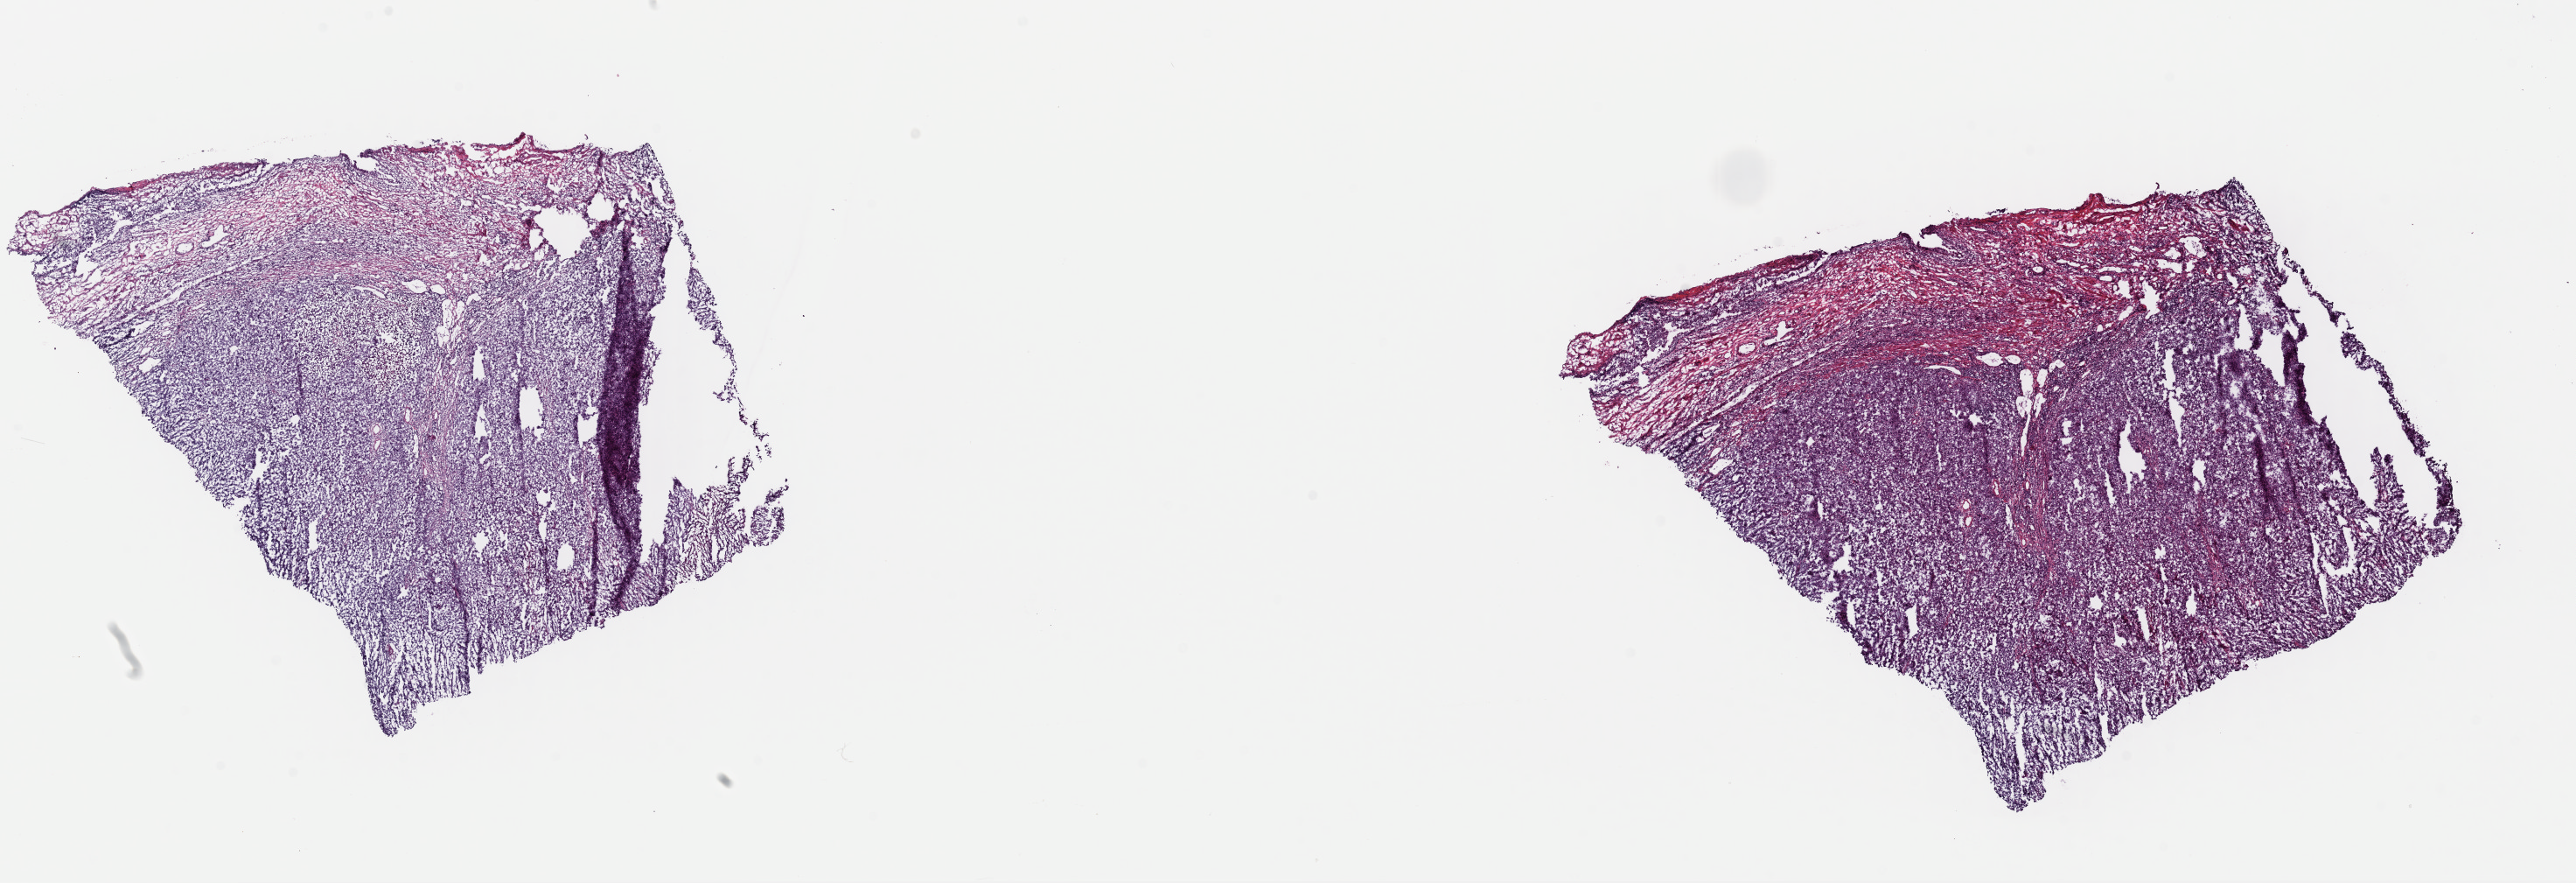
Whole-slide histology image, H&E-stained — whole scanned area (about 23.3 x 8.0 mm) shown as a low-resolution overview, frozen section, bladder, primary tumour sample. Male patient; age at initial diagnosis 75 years.
Pathologic diagnosis: Transitional cell carcinoma (posterior wall of bladder).